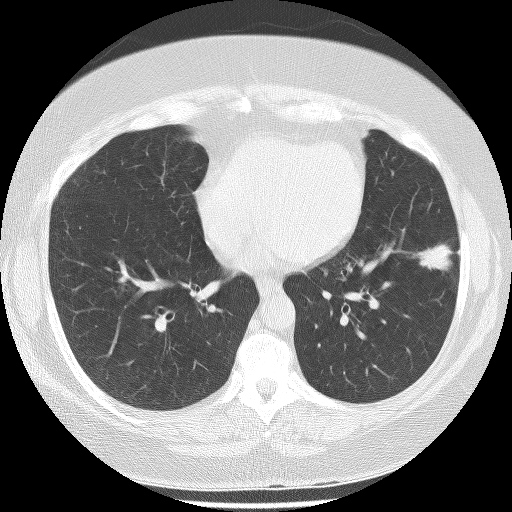
Low-dose screening chest CT, axial slice, baseline screening round, lung window (W 1500 / L -600 HU), 120 kVp, 512 × 512 image matrix, field of view 340 × 340 mm. Female, age 56 years at enrolment.
- Lesion marked by an expert reader, bounding box [x1, y1, x2, y2] px = [397, 229, 463, 282].
- Reader record for this screening exam (exam-level; its link to the box is not recorded): non-calcified nodule or mass ≥4 mm, left lower lobe, 22 × 17 mm, spiculated (stellate) margins, soft tissue attenuation.
- Official screen result: positive, change unspecified: nodule(s) >= 4 mm or enlarging nodule(s), mass(es), or other non-specific abnormalities suspicious for lung cancer.
- Participant outcome: lung cancer diagnosed 63 days after this screen — bronchiolo-alveolar adenocarcinoma, NOS, left lower lobe, stage IA (AJCC 6th edition), 18 mm at pathology.